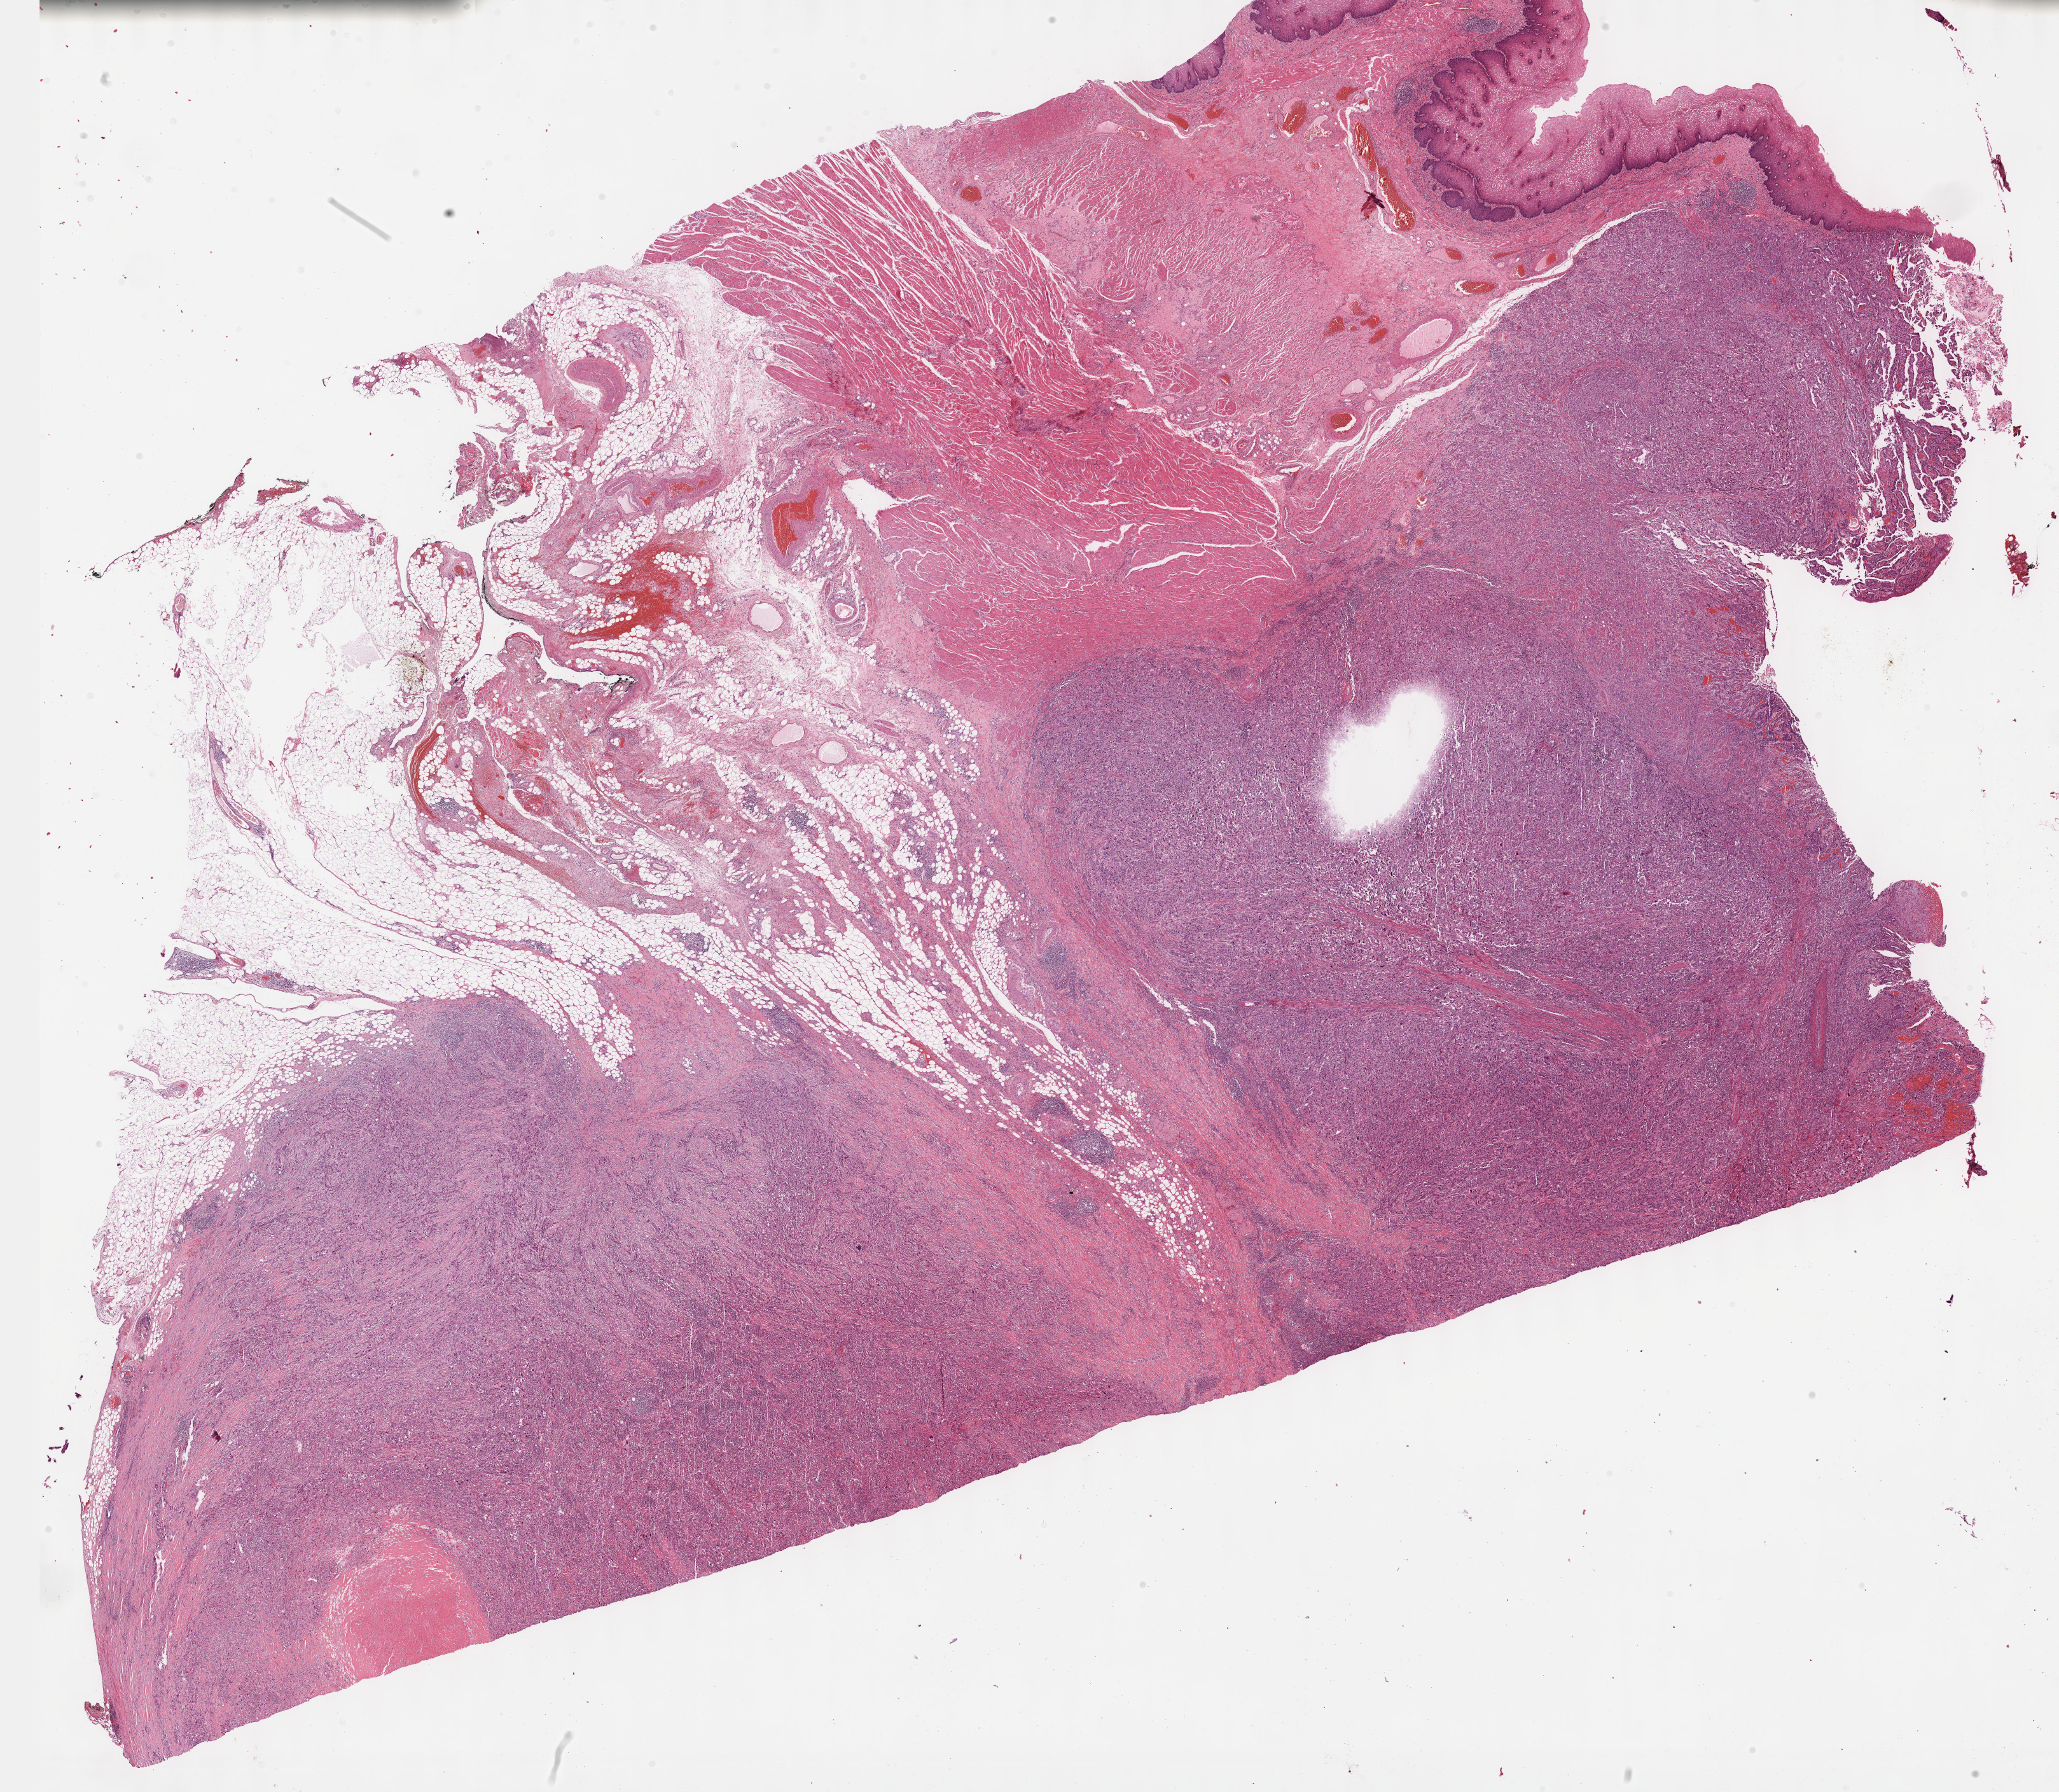
Whole-slide histology image, H&E, whole scanned area (about 26.2 x 22.8 mm) shown as a low-resolution overview, formalin-fixed paraffin-embedded (FFPE) diagnostic section, primary tumour sample from the esophagus. Male, age 60 years at initial diagnosis.
Diagnosis: Squamous cell carcinoma, NOS (lower third of esophagus).